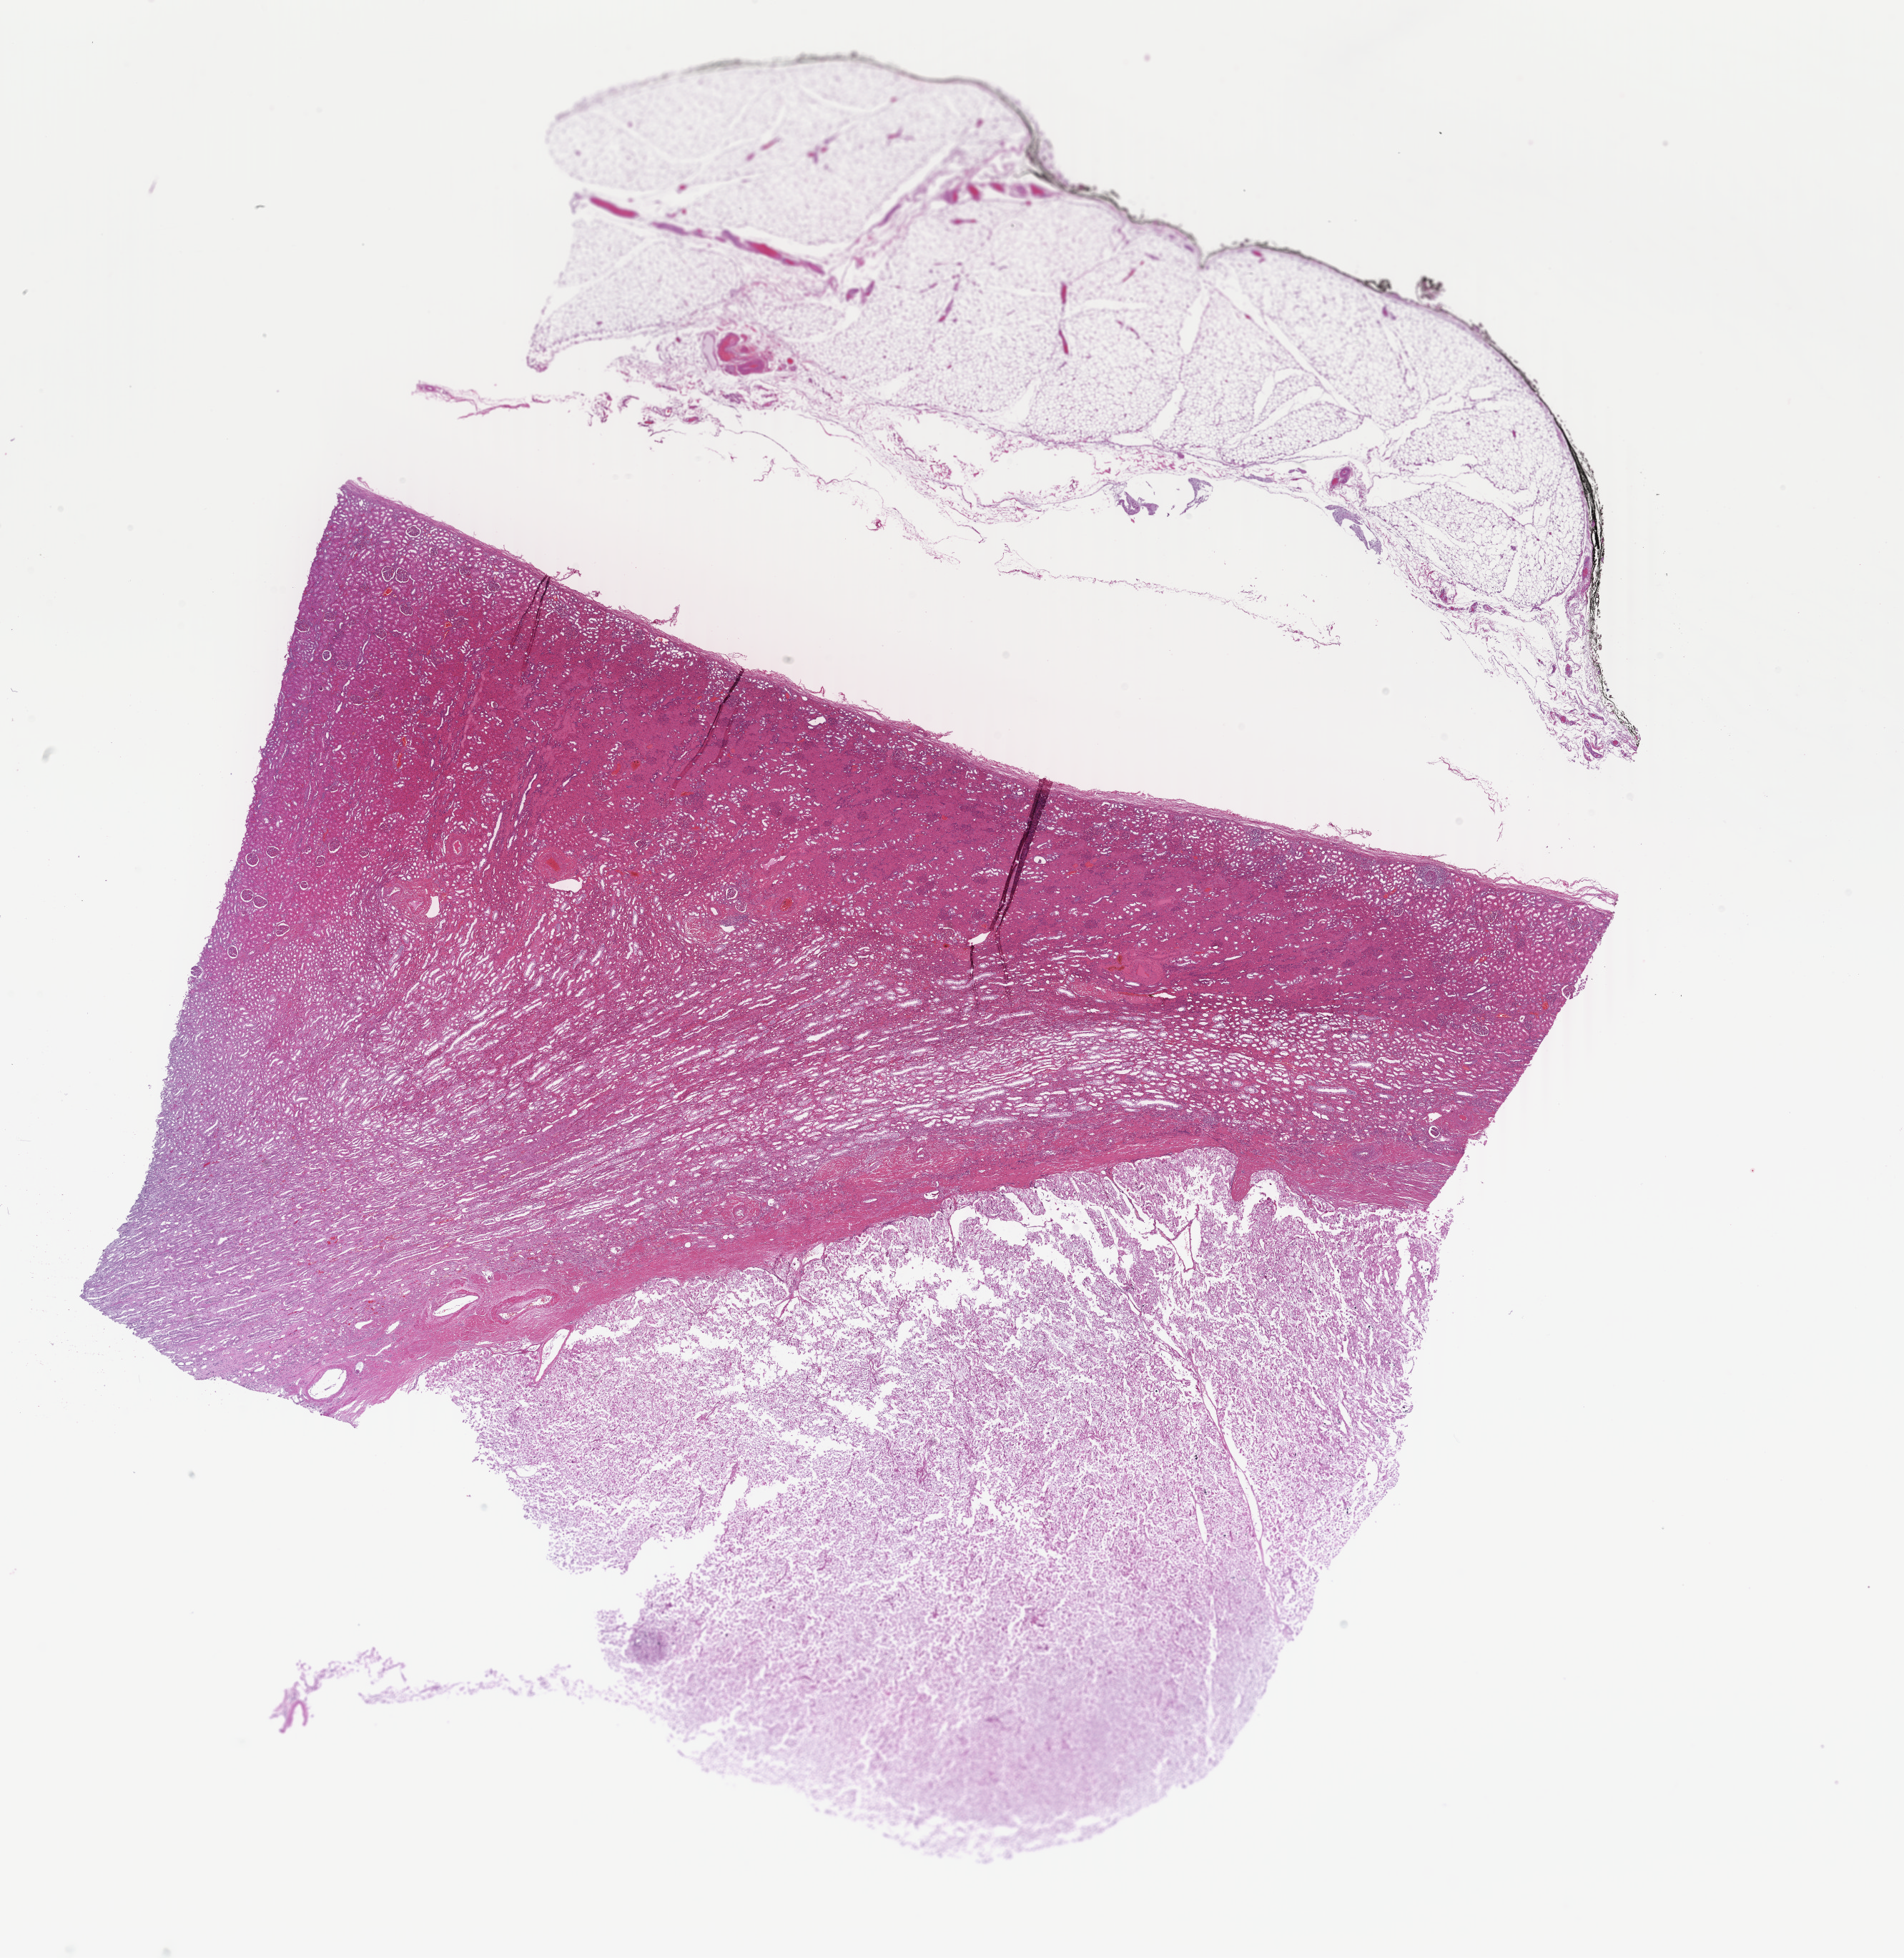
H&E whole-slide image, low-resolution overview of the scanned area, about 21.2 x 21.8 mm (from a 40x scan), formalin-fixed paraffin-embedded (FFPE) diagnostic section, kidney, primary tumour sample. Male, age 47 years at initial diagnosis.
Pathologic diagnosis: Renal cell carcinoma, chromophobe type. AJCC pathologic stage: I (5th edition).